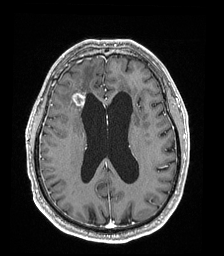
Brain MRI from a brain-tumour surgery series, one axial slice; position 78 of 192 along the scan axis; T1-weighted post-contrast; 1 mm slice thickness; 224 × 256 image matrix, field of view 224 × 256 mm. From the clinical record (not read from this slice): histopathology: Astrocytoma; WHO grade: 4; IDH mutation: yes.
Annotated regions visible in this slice (outlined manually by an expert reader):
- tumour: bounding box [x1, y1, x2, y2] px = [72, 93, 85, 107]